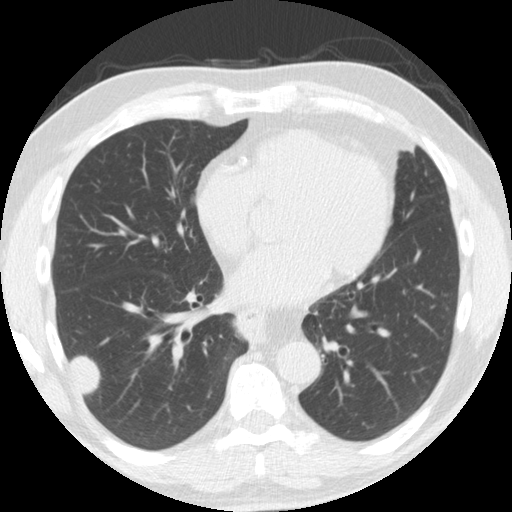
Low-dose screening chest CT, one axial slice; slice 73 of 174 in the series (ordered by position); reconstruction kernel STANDARD; 120 kVp; lung window (W 1500 / L -600 HU); 2.5 mm slice thickness; 512 × 512 image matrix, field of view 341 × 341 mm.
Outlined on this slice (manually delineated by an expert):
- lesion 1 (tumor, lower lobe of right lung): box from (x=70, y=355) to (x=100, y=394) px